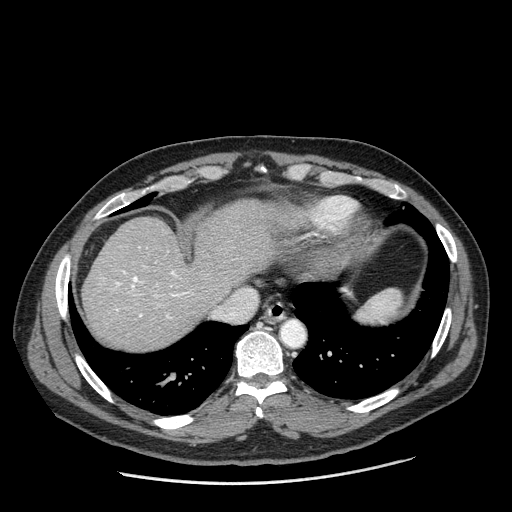
Contrast-enhanced abdominal CT (liver protocol), one axial slice; position 163 of 198 along the scan axis; reconstruction kernel STANDARD; 120 kVp; one of 2 acquisitions stored at this slice position; soft-tissue window (W 400 / L 40 HU); 2.5 mm slice thickness; 512 × 512 image matrix, field of view 400 × 400 mm. From the clinical record (not read from this slice): diagnosis: hepatocellular carcinoma (patient treated with transarterial chemoembolisation; whether this scan precedes or follows treatment is not stated here); TNM stage (as recorded): Stage-II; Child-Pugh class: A; tumour differentiation: moderately differentiated; tumour nodularity: multinodular.
Annotated regions visible in this slice (semi-automatically segmented with operator editing):
- abdominal aorta: box from (x=282, y=321) to (x=304, y=345) px
- liver parenchyma outside the tumour (the mass and vessels are separate outlines, so this box may not span the whole liver): (x=82, y=200)–(x=280, y=350)
- liver vessels: (x=115, y=261)–(x=190, y=319)